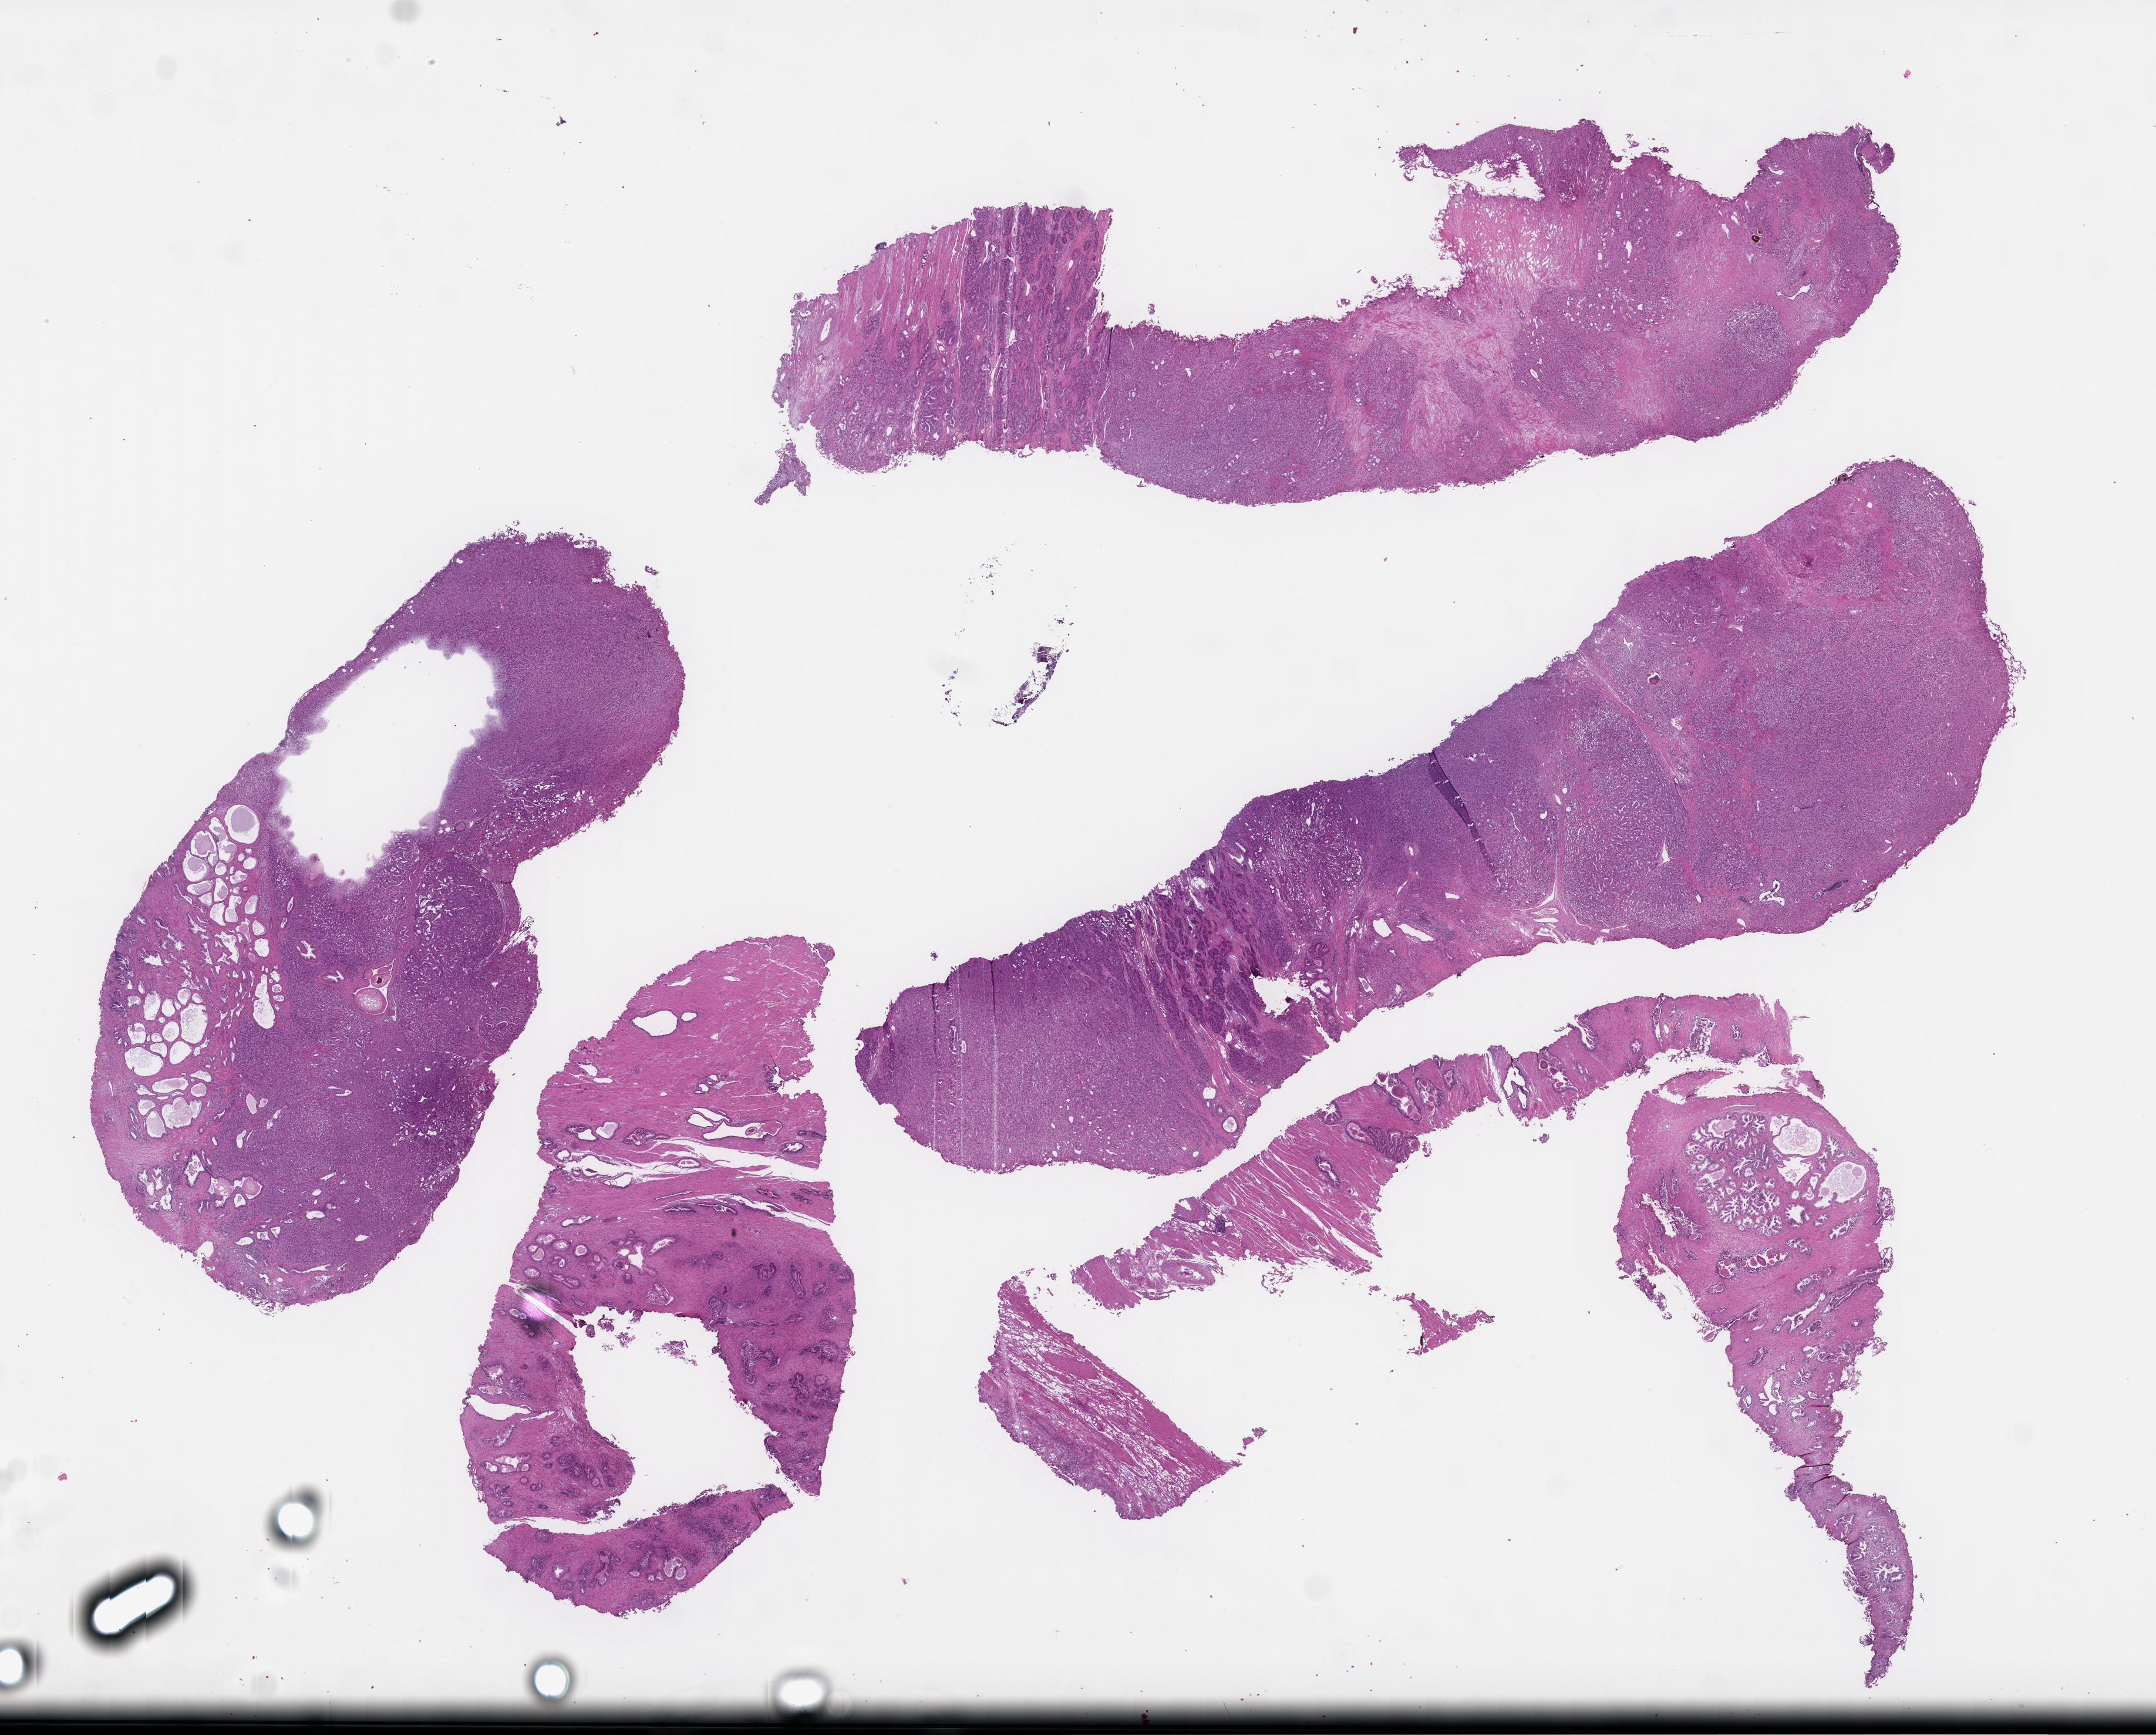
Whole-slide image, hematoxylin and eosin (H&E) stain, whole scanned area (about 29.7 x 23.9 mm) shown as a low-resolution overview, formalin-fixed, paraffin-embedded (FFPE) tissue, tissue site: prostate. Male patient.
* this section: primary tumour tissue
* diagnosis: Prostate Carcinoma